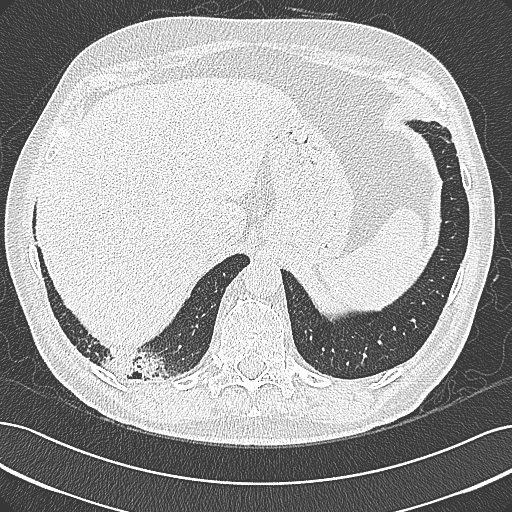
Low-dose screening chest CT, axial slice. Baseline annual screen. Lung window (W 1500 / L -600 HU). 1 mm slice thickness. Lung (sharp) reconstruction kernel (B80f). Slice 257 of 355 in the series. 512 × 512 image matrix. Male, age 68 years at enrolment. Former smoker at enrolment.
- Expert reader's lesion annotation, box from (x=94, y=337) to (x=195, y=397) px.
- Screening reader's record for this exam: no non-calcified nodule ≥4 mm recorded.
- Lung cancer was diagnosed 154 days after this screen: mucinous adenocarcinoma, right lower lobe, well differentiated (G1), stage IB (AJCC 6th edition), 50 mm at pathology.